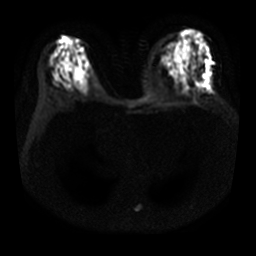
Breast MRI, one axial slice. Slice 14 of 29 in the series (ordered by position). Diffusion-weighted series; image 2 of 4 stored at this slice position (different b-values; order by instance number). 3 T. 5 mm slice thickness. 256 × 256 image matrix, field of view 340 × 340 mm. Female patient.
Structures marked on this image (expert manual segmentation):
- tumour on diffusion-weighted imaging: bounding box [x1, y1, x2, y2] px = [203, 74, 206, 78]